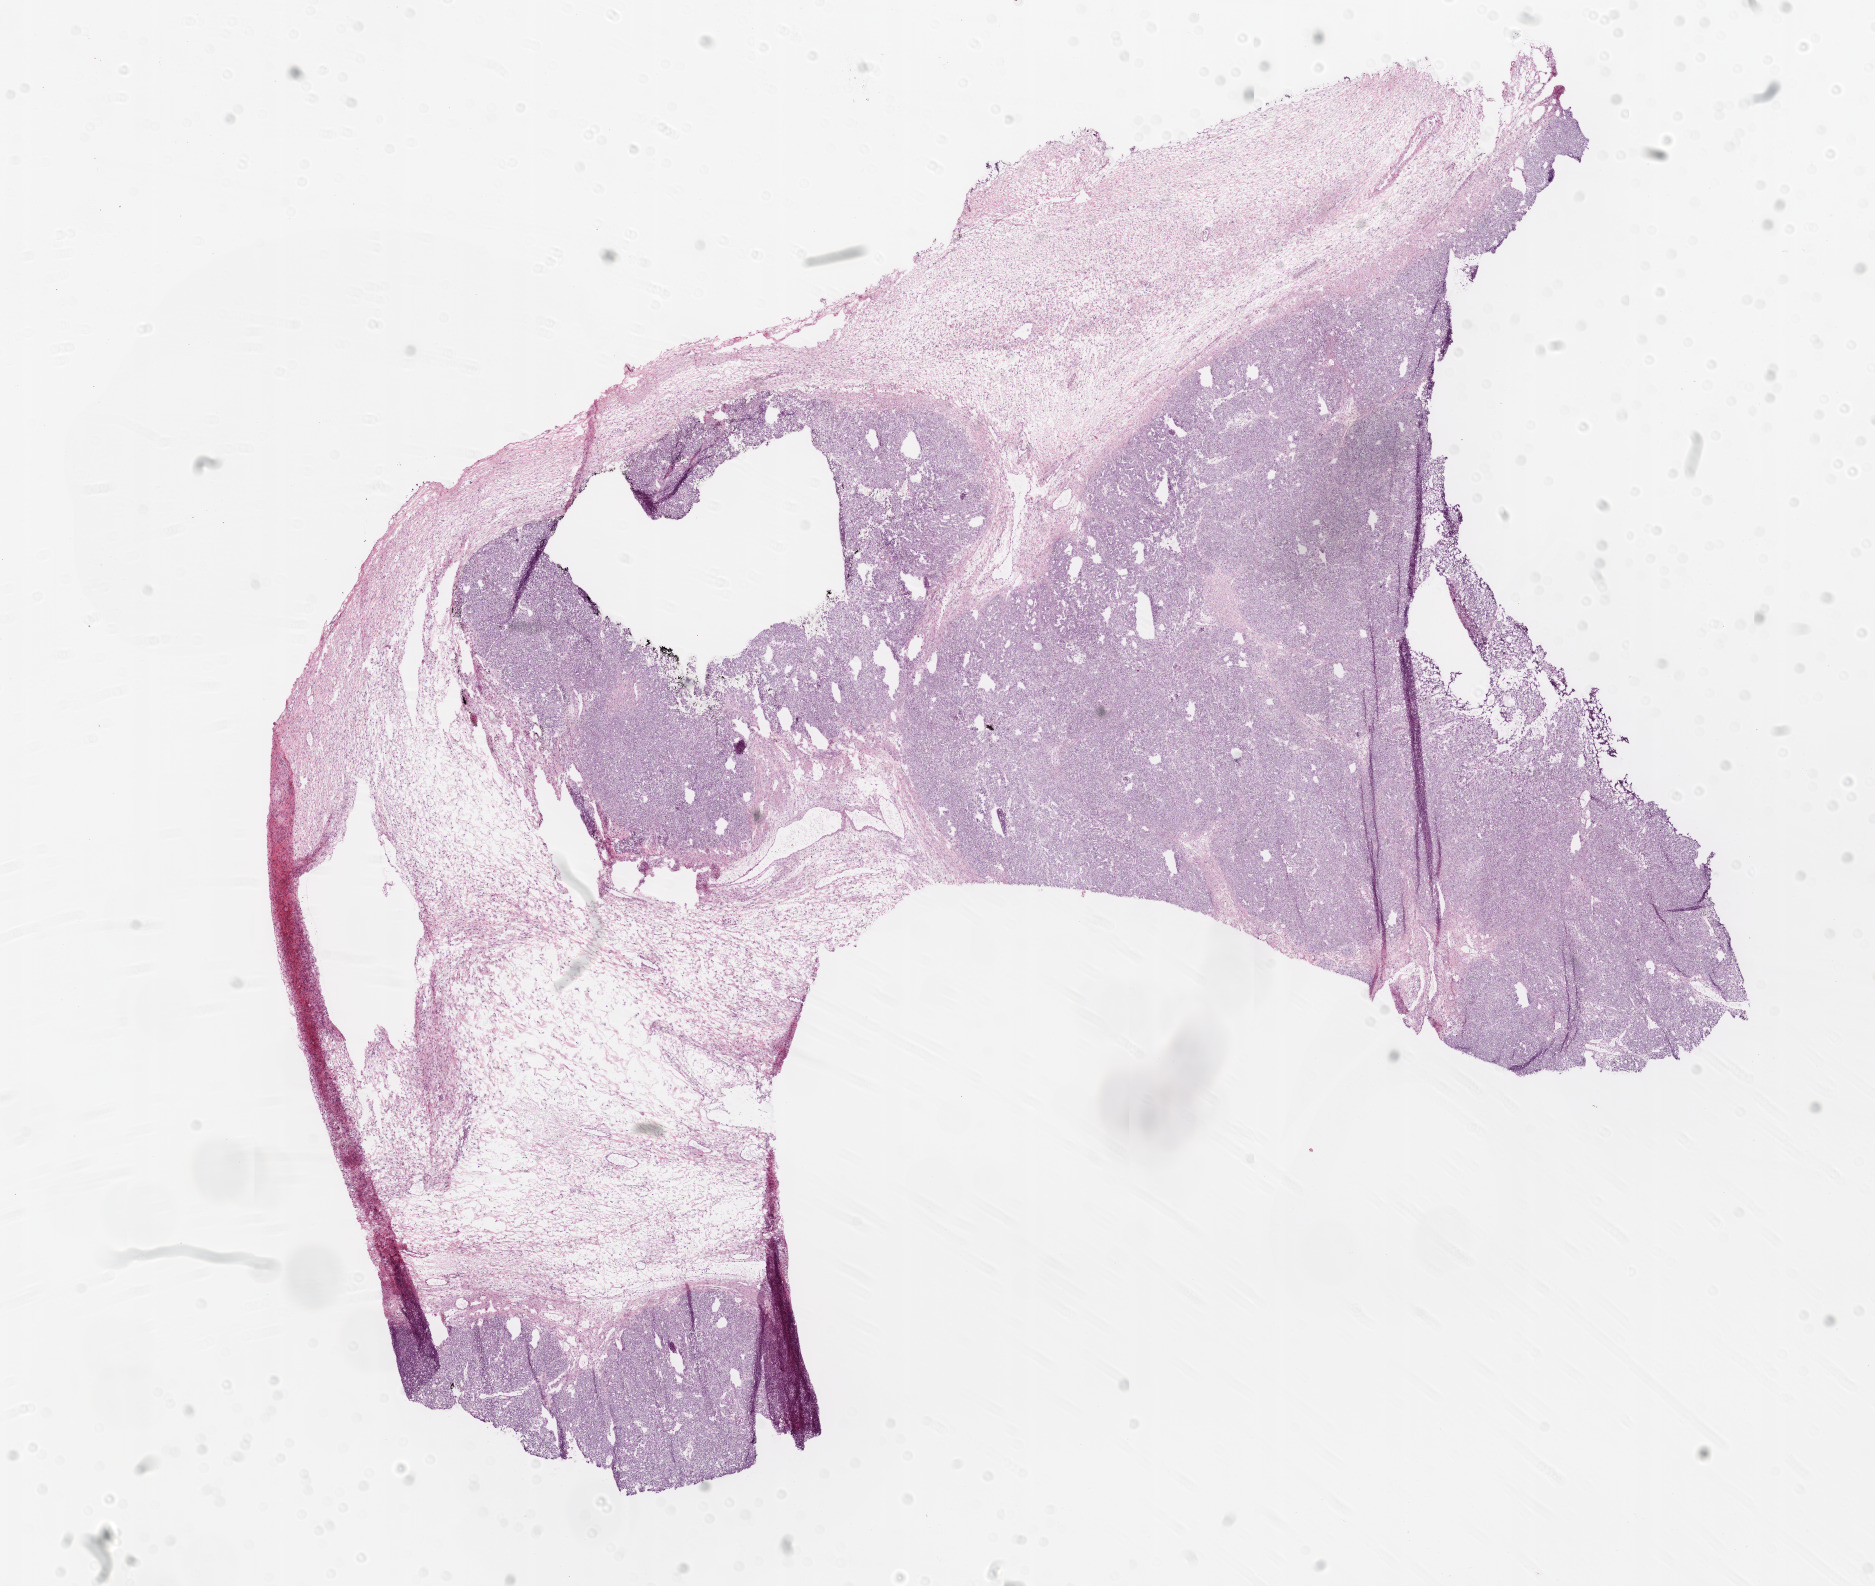
Digitized Hematoxylin and eosin (H&E) stained tissue section (whole slide), shown as a low-resolution overview of the whole scanned area (about 15.0 x 12.7 mm). Frozen section from the bottom of the tissue portion. Sample: primary tumour, ovary. Female patient; age at initial diagnosis 63 years.
Pathologic diagnosis: Serous cystadenocarcinoma, NOS.